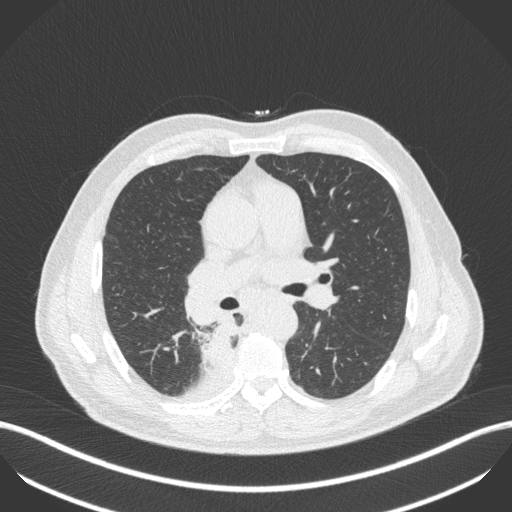
Chest CT, one axial slice. Slice 269 of 451 in the series (ordered by position). Reconstruction kernel B31f. 100 kVp. Lung window (W 1500 / L -600 HU). 512 × 512 image matrix, field of view 400 × 400 mm. Patient: male, 61 years. Case-level facts recorded for this patient, not image findings: clinical TNM (as recorded): T1 N0 M0; histopathological grade: G3.
Outlined on this slice (rectangle marked by the reading radiologist):
- lung tumour (recorded histology: small cell carcinoma): bounding box (x1, y1, x2, y2) in pixels: (203, 318, 241, 367)